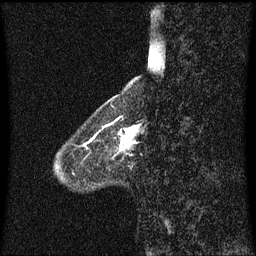
Breast MRI (dynamic contrast-enhanced), one sagittal slice; slice 18 of 60 in the series (ordered by position); dynamic contrast-enhanced series, image 2 of 3 at this slice position (ordered by acquisition); 1.5 T; TE 4.2 ms, TR 8.4 ms; 2 mm slice thickness; 256 × 256 image matrix, field of view 200 × 200 mm. Female patient, age 58 years.
Annotated regions visible in this slice (semi-automatic segmentation, software-assisted and operator-edited):
- analysis volume of interest (the breast-tissue region the enhancement analysis was run in; not a lesion): bounding box [x1, y1, x2, y2] px = [102, 120, 139, 160]
- tumour enhancement mask (voxels above the 70 % enhancement threshold inside the analysis volume of interest): [102, 121, 139, 151]